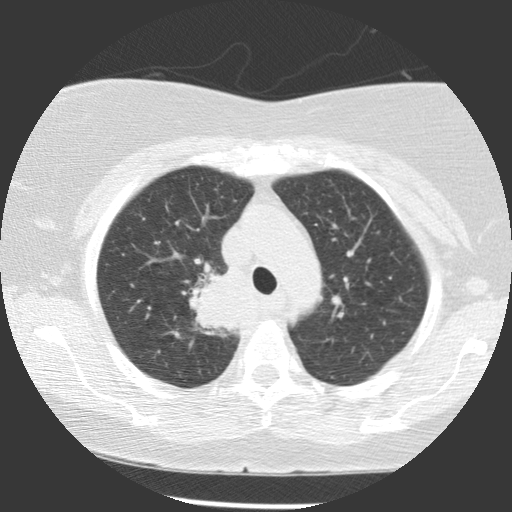
Low-dose screening chest CT, one axial slice; slice 87 of 116 in the series (ordered by position); reconstruction kernel STANDARD; 140 kVp; lung window (W 1500 / L -600 HU); 512 × 512 image matrix, field of view 320 × 320 mm.
Annotated regions visible in this slice (manually delineated by an expert):
- lesion 1 (tumor, upper lobe of right lung): bounding box (x1, y1, x2, y2) in pixels: (188, 268, 240, 337)